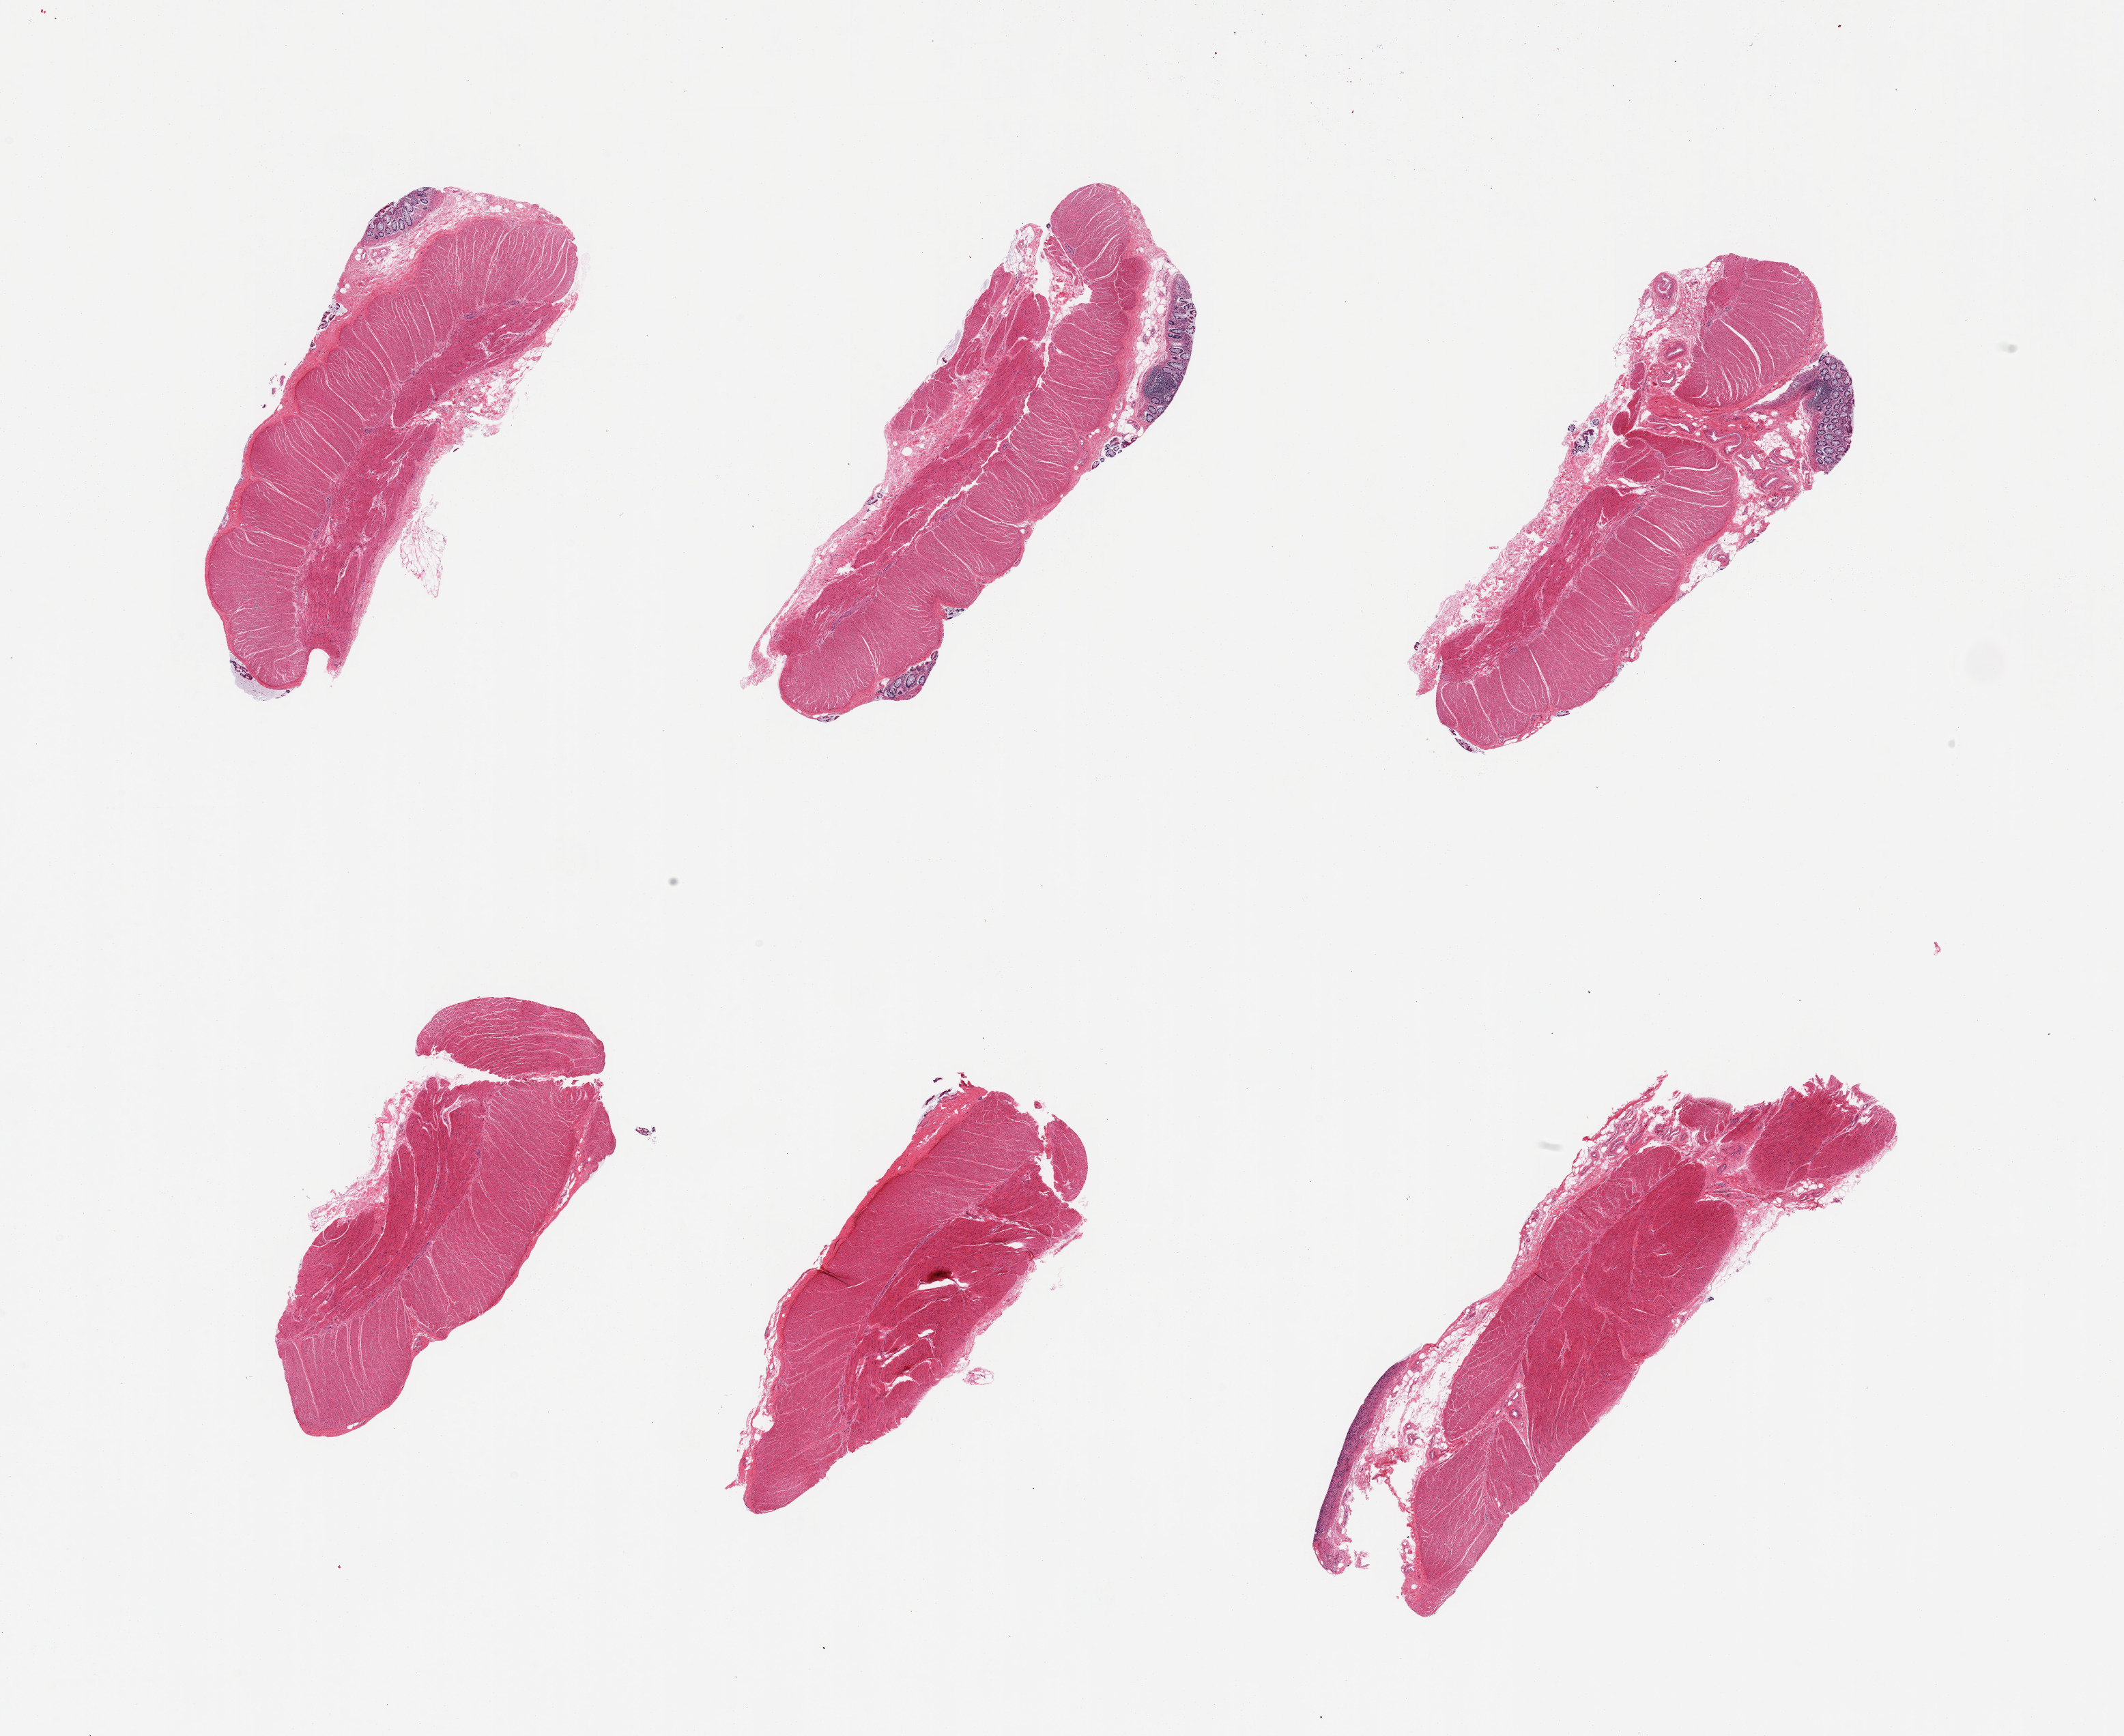
Whole-slide image, haematoxylin and eosin stain, brightfield — shown as a low-resolution overview of the whole scanned area (about 24.6 x 20.1 mm, slide scanned at 20x), PAXgene-fixed, paraffin-embedded tissue, target tissue: sigmoid colon, tissue donor sample. Male donor.
Reviewer comment on this tissue sample: 6 pieces; predominantly muscularis, several pieces include strips of residual mucosa.